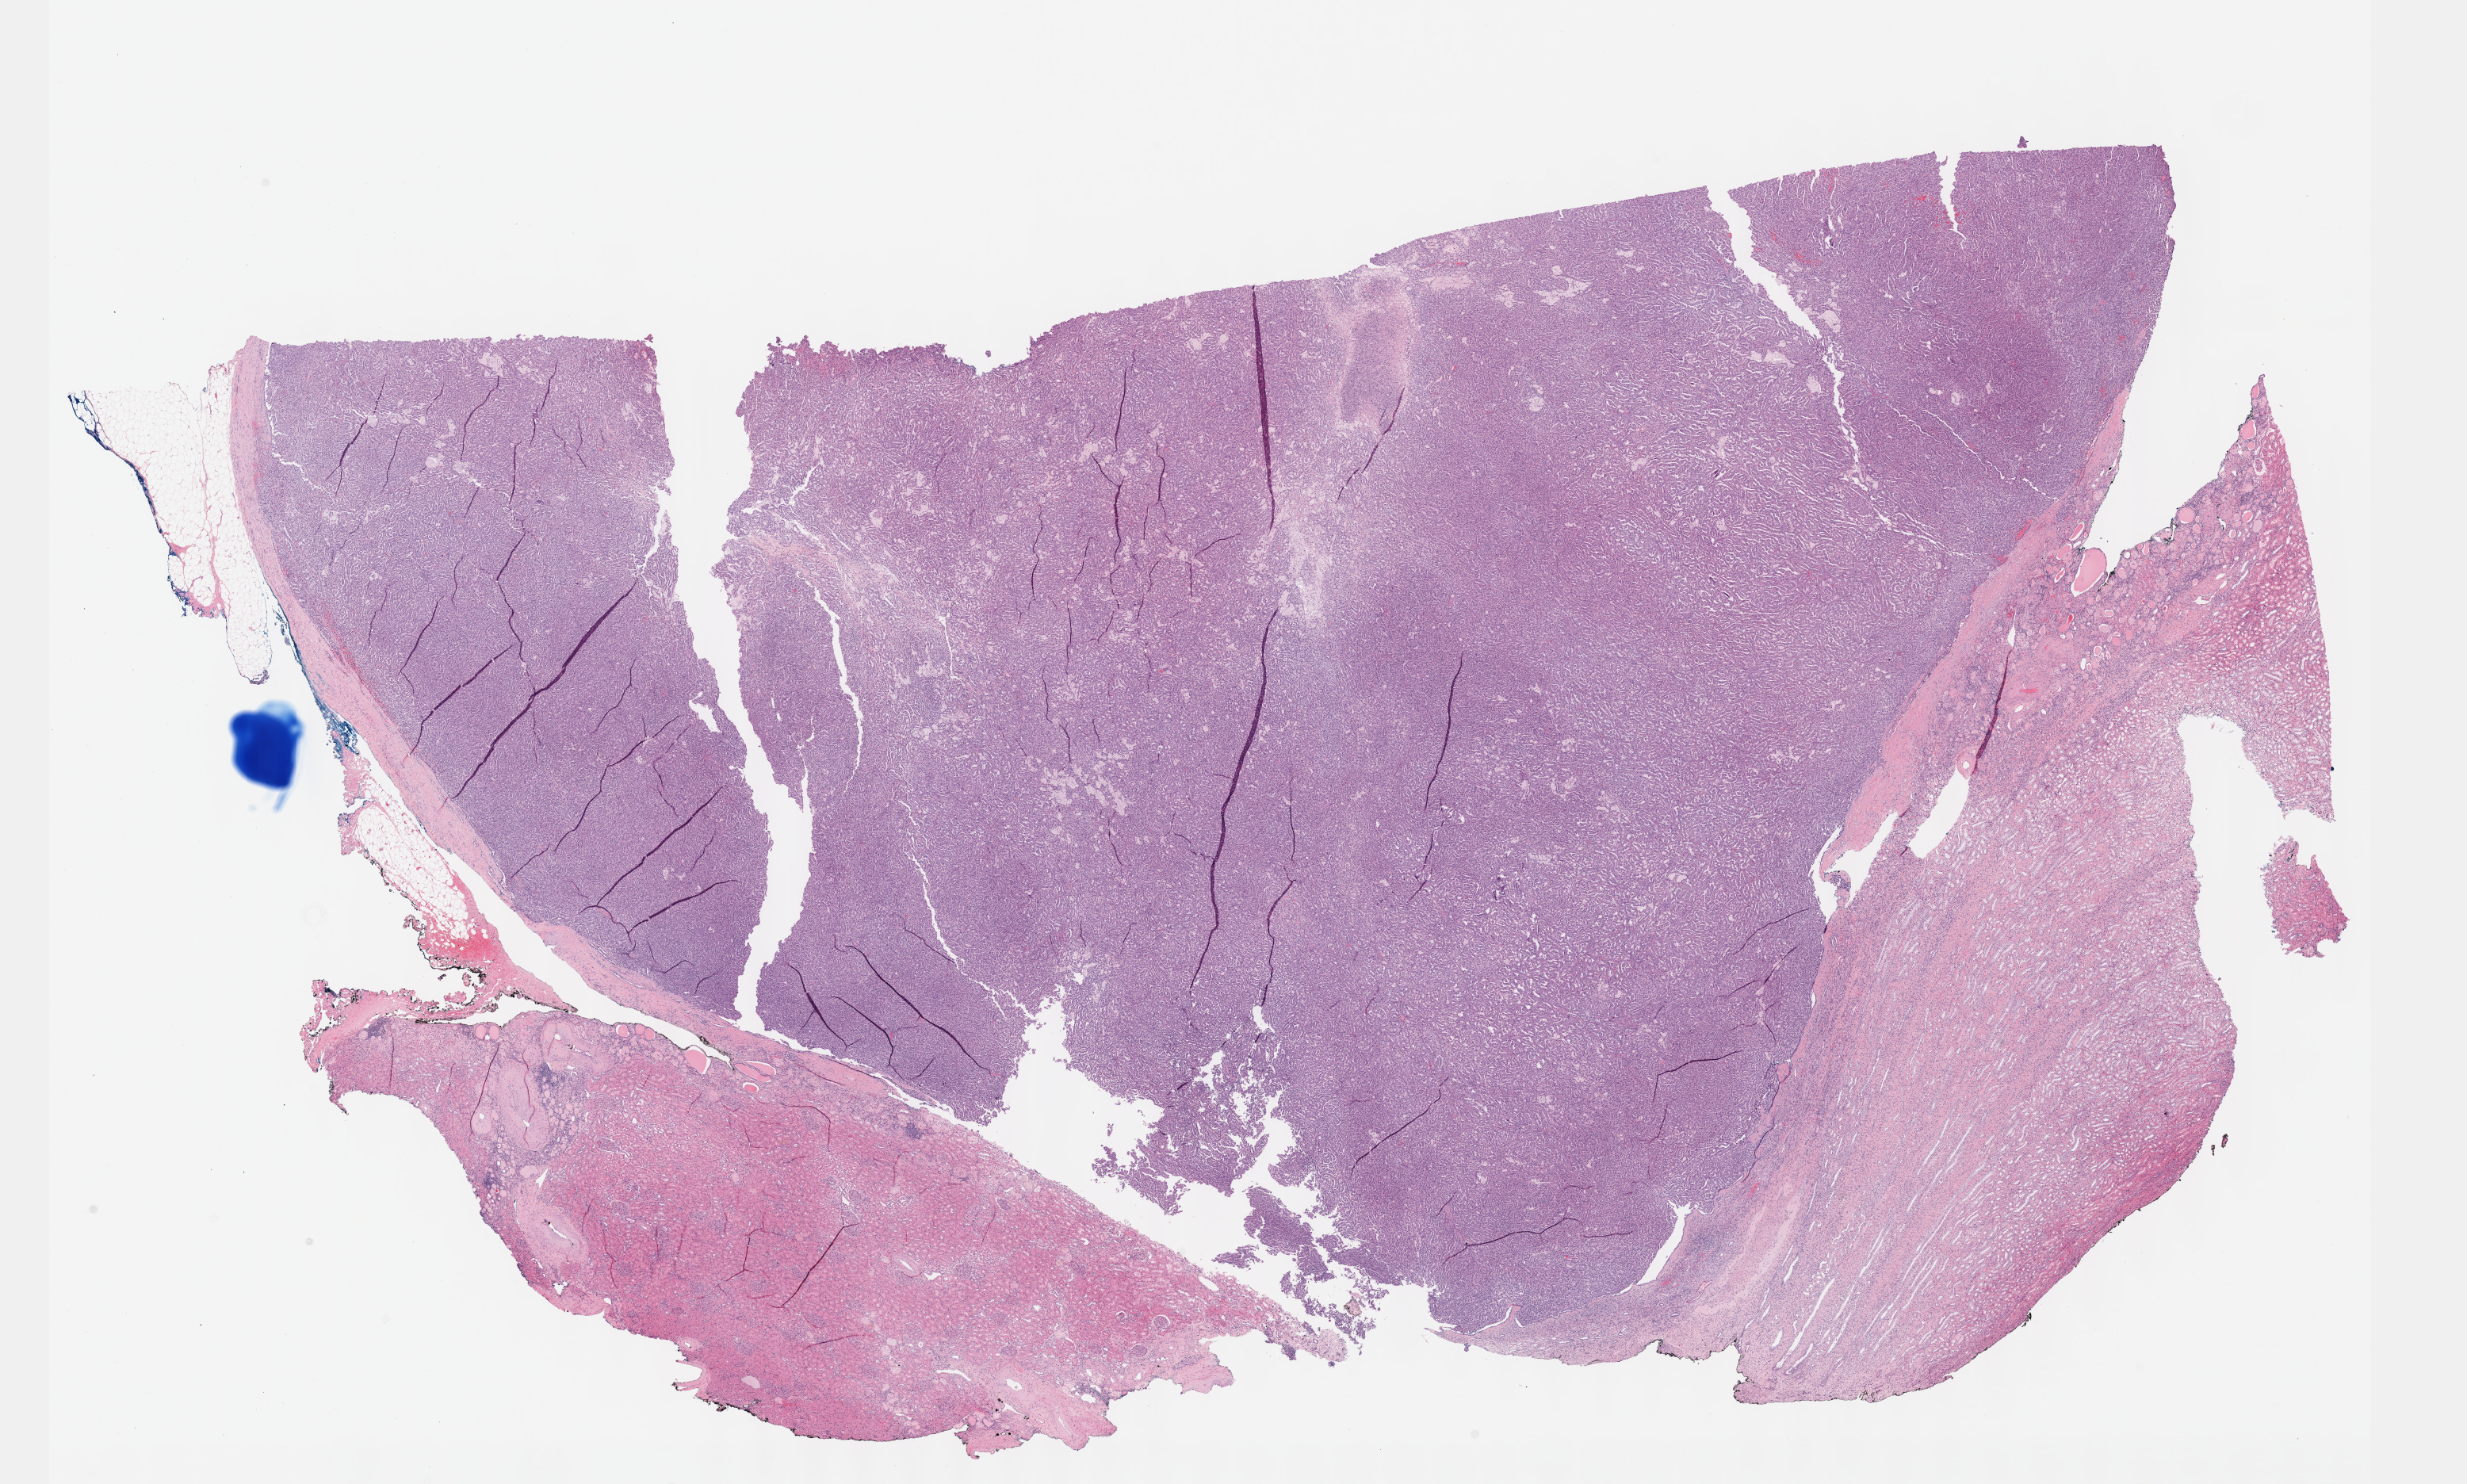
Whole-slide histology image, Hematoxylin and eosin (H&E) stained, a low-resolution overview of the entire scanned area, about 25.1 x 15.1 mm, formalin-fixed paraffin-embedded (FFPE) diagnostic section, primary tumour sample from the kidney. Patient: male, age at initial diagnosis 65 years.
Pathologic diagnosis: Papillary adenocarcinoma, NOS. TNM: T3a NX MX. AJCC pathologic stage: III. Laterality: right.